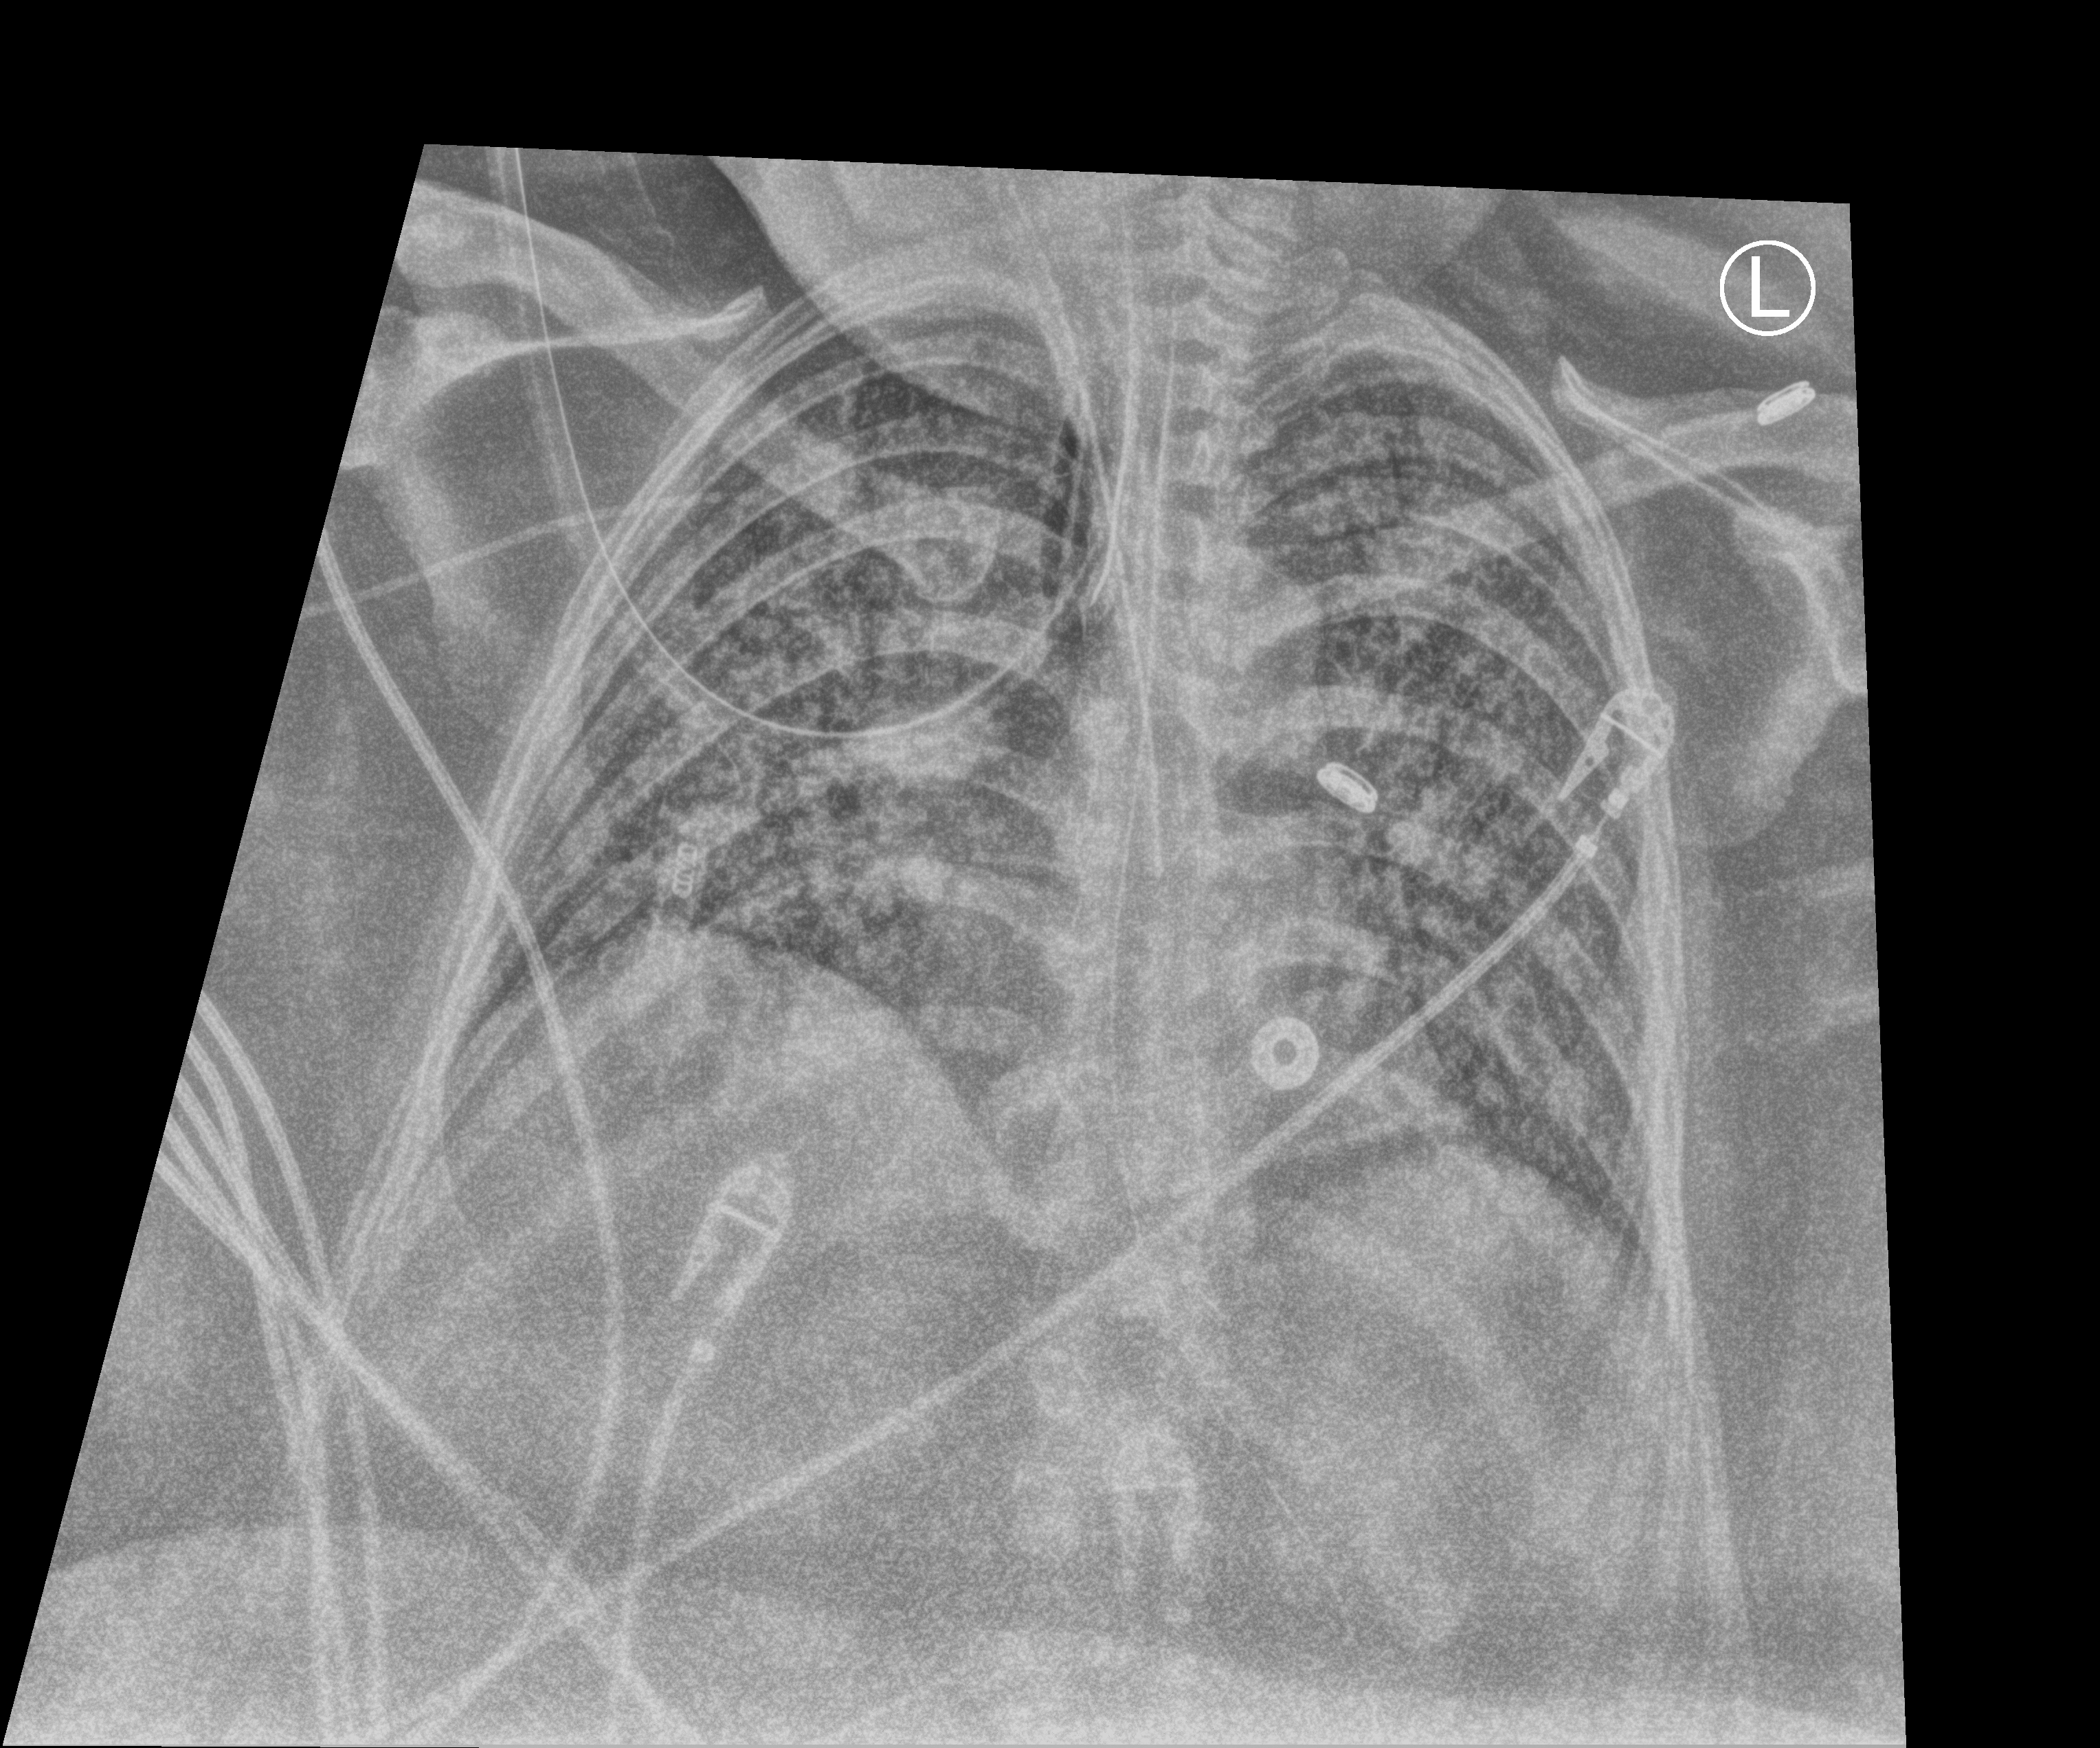
Portable chest radiograph, anteroposterior (AP) projection. Patient hospitalised with COVID-19; female, aged 18–59 years.
From the hospital-stay record, not from the radiograph (when in the stay this image was taken is not recorded): admitted to intensive care during this hospital stay: yes.